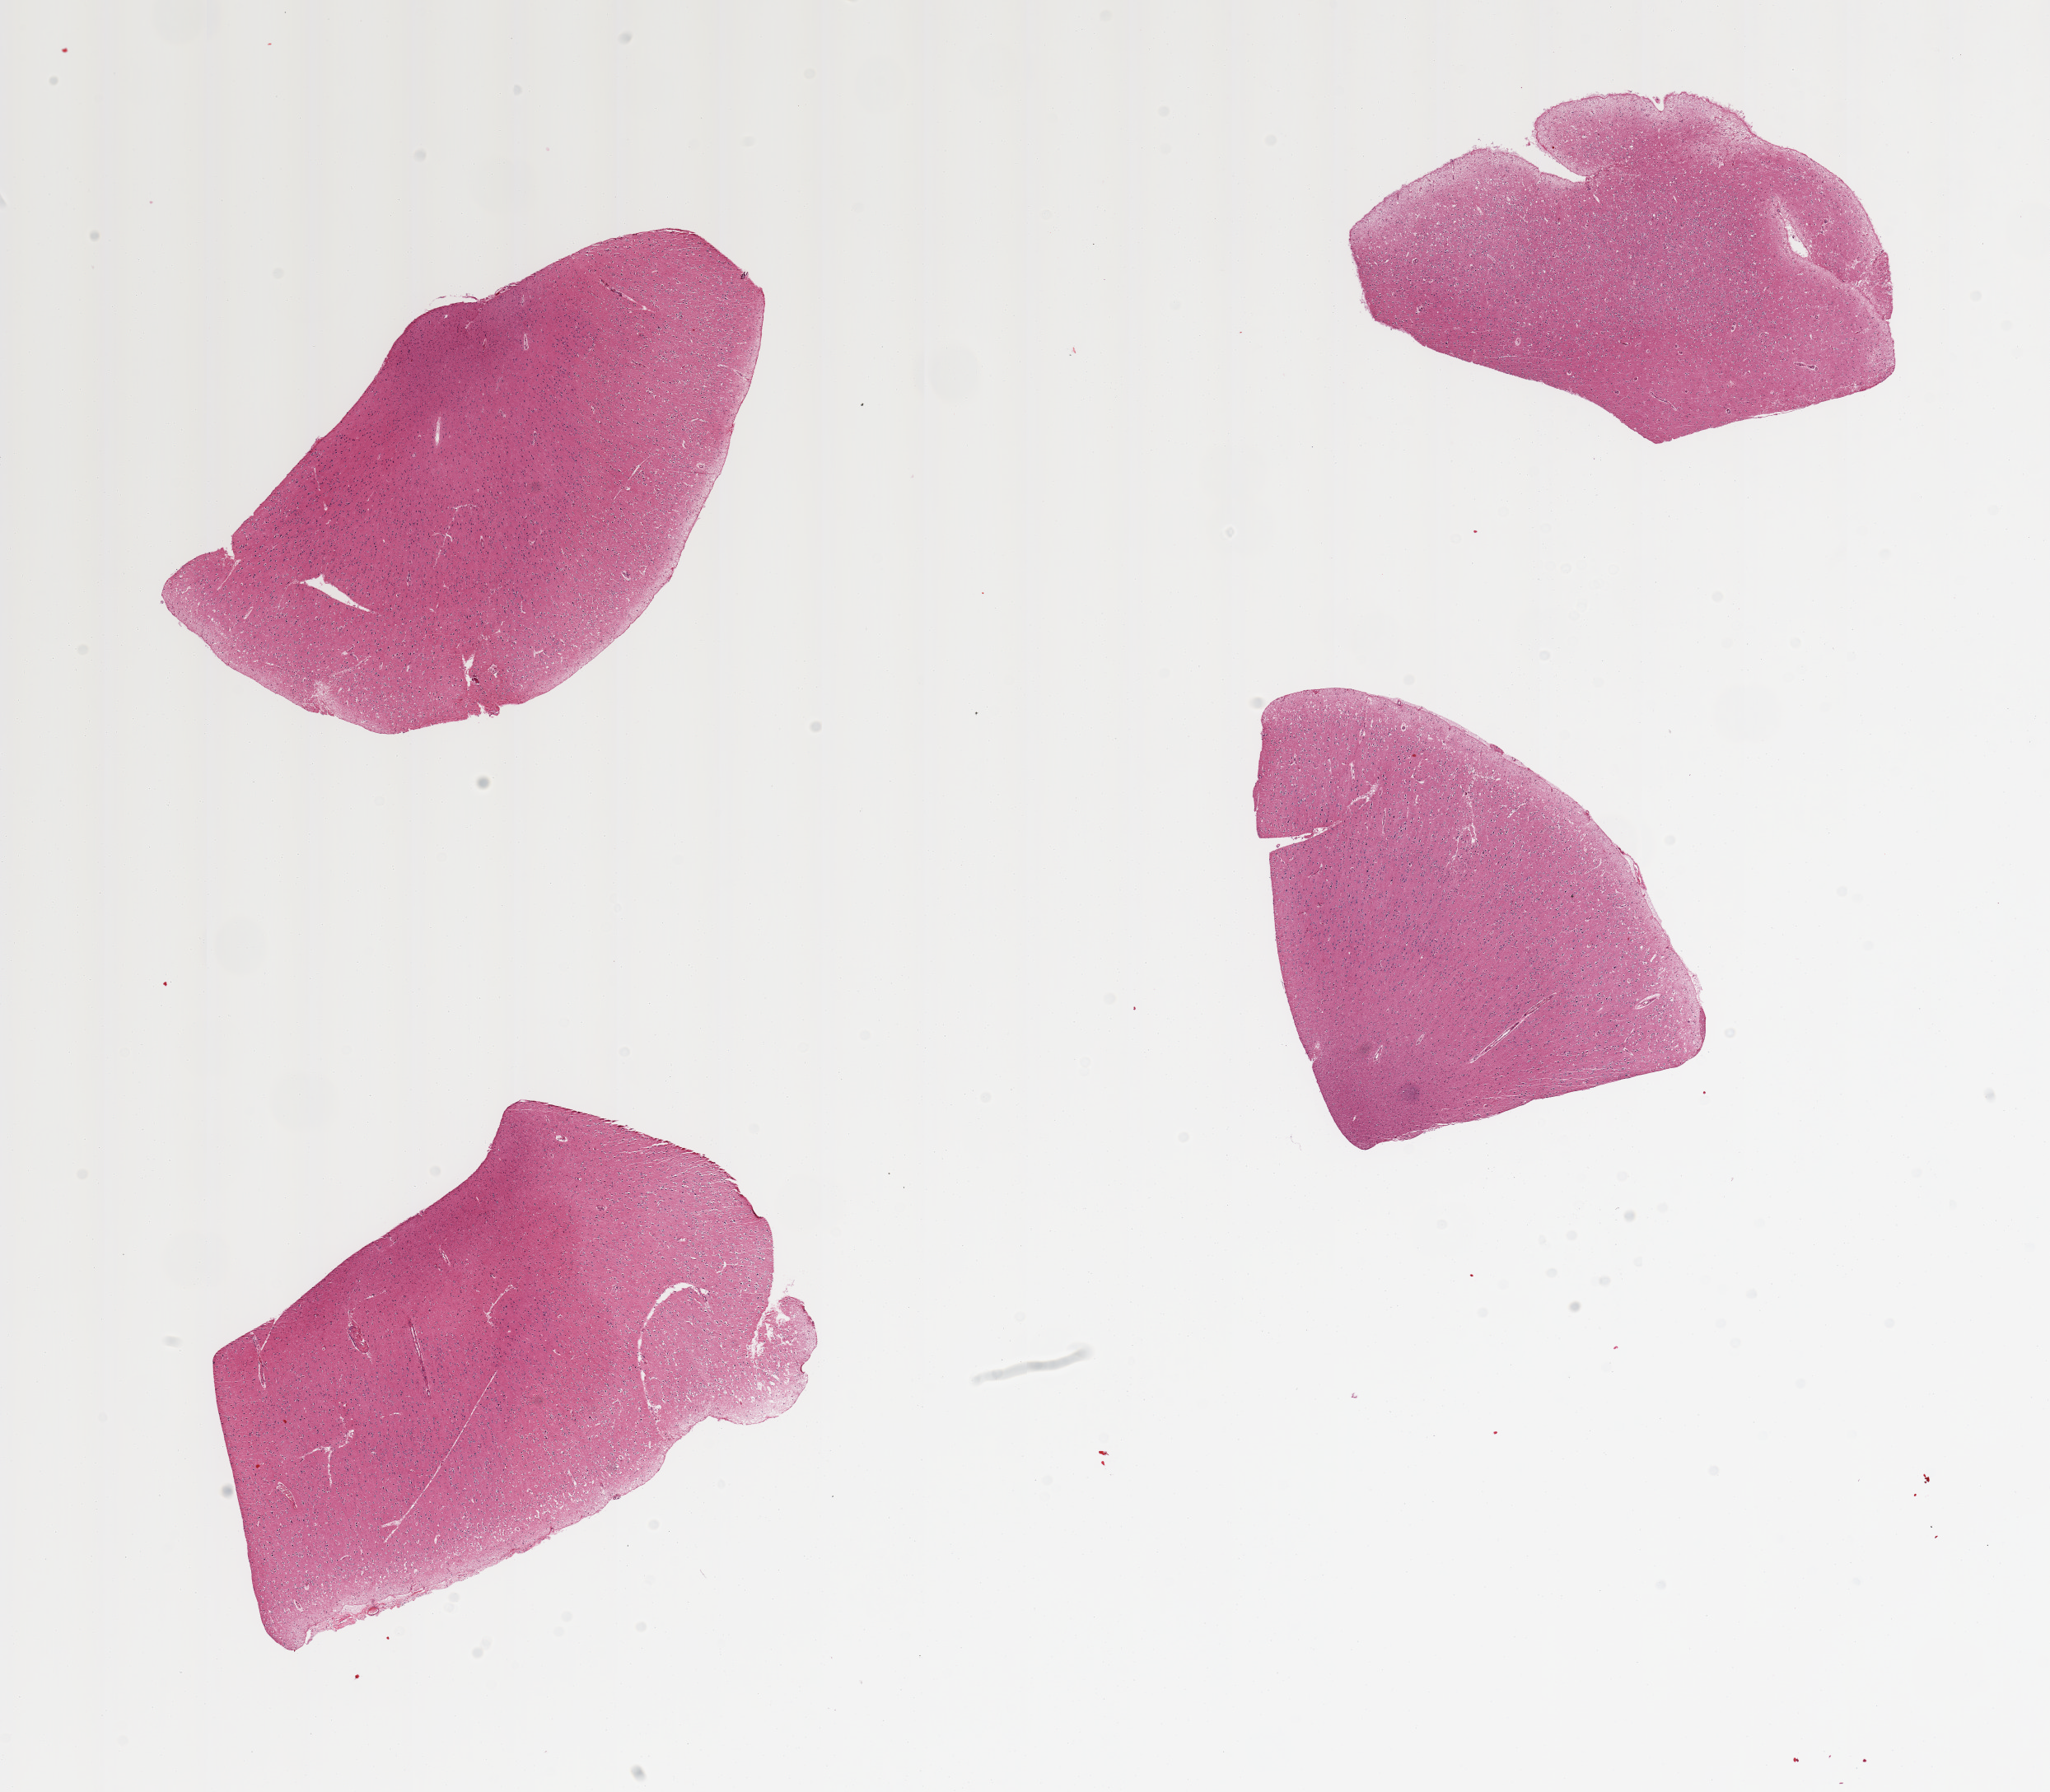
Haematoxylin and eosin whole-slide image — low-resolution overview of the scanned area, about 19.7 x 17.2 mm; PAXgene-fixed paraffin-embedded (PFPE) section; sampled site (target tissue): cerebral cortex; donor tissue sample. Donor: male.
• reviewer comment on this tissue sample: 4 pieces, no abnormalities